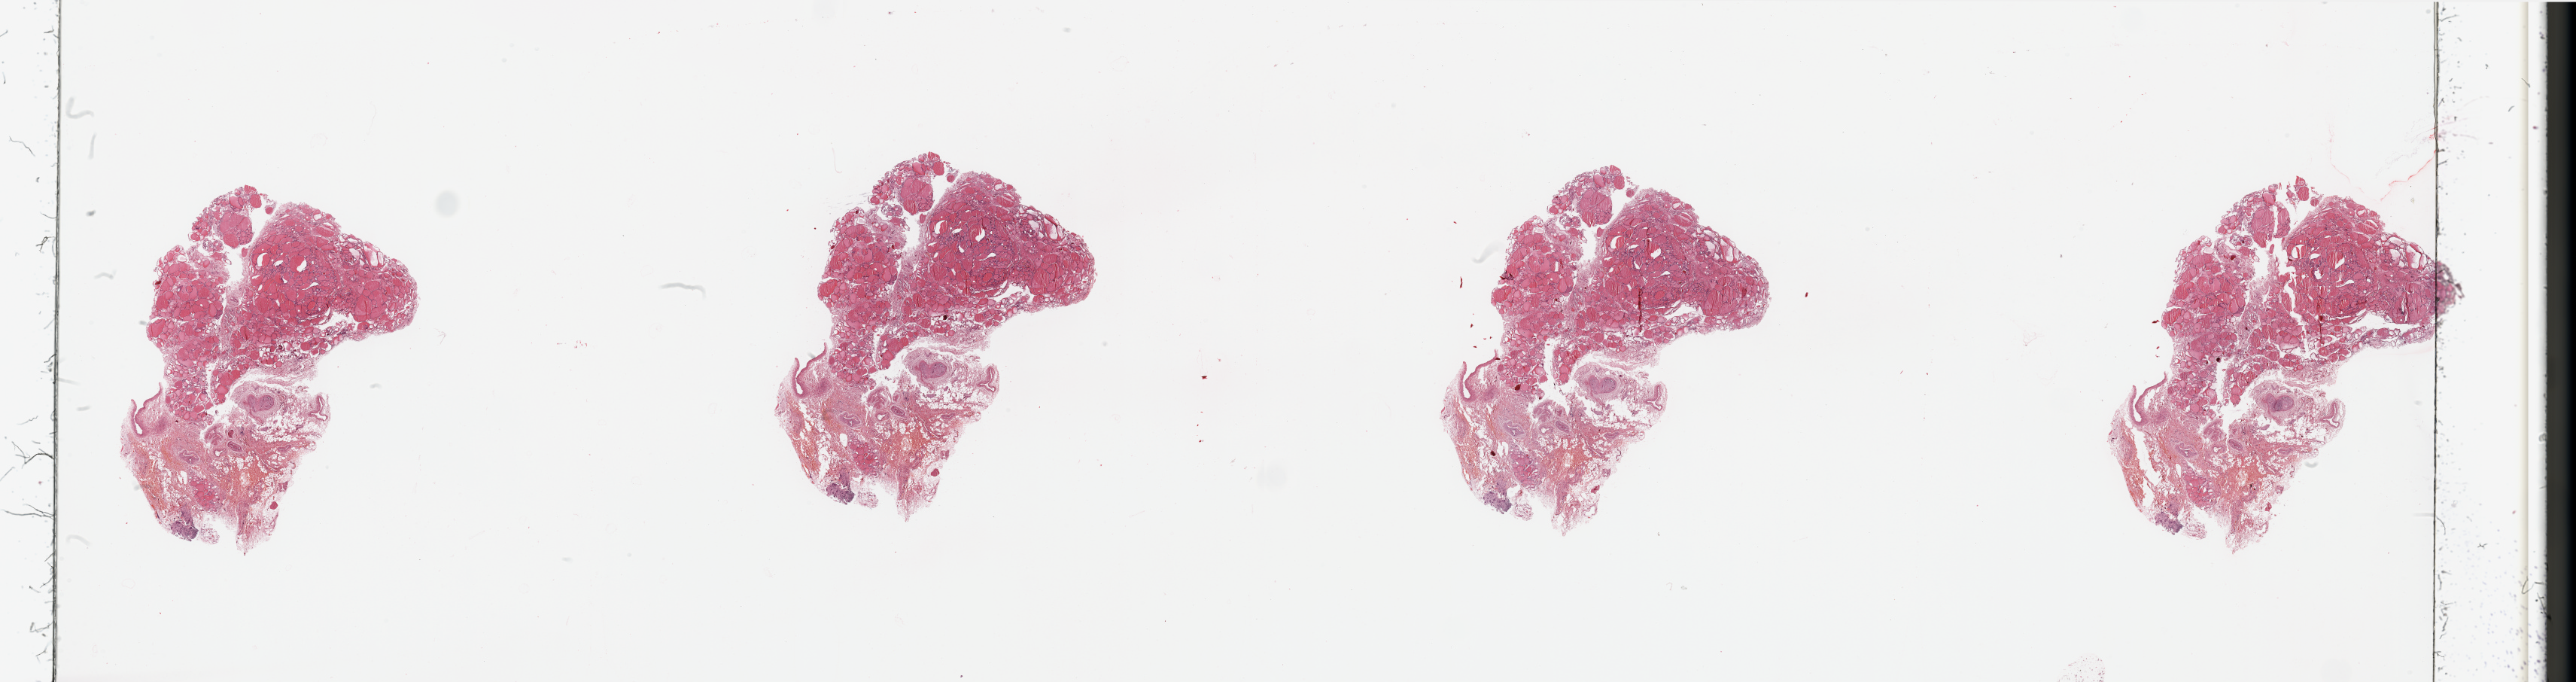
H&E-stained whole-slide image, whole scanned area (about 54.1 x 14.3 mm, slide scanned at 20x) shown as a low-resolution overview. Head and neck, tissue type not recorded. Male, 81 y/o.
* patient diagnosis: Squamous cell carcinoma, NOS